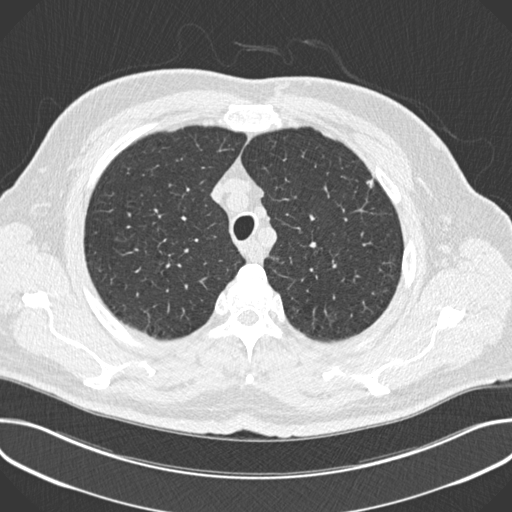
Chest CT (low-dose screening protocol), one axial image. Baseline screening round. Lung window (W 1500 / L -600 HU). 2 mm slice thickness. Standard (soft-tissue) reconstruction kernel (B30f). Slice 51 of 245 in the series. 512 × 512 image matrix, field of view 380 × 380 mm. Male participant, aged 63 years at enrolment. Current smoker at enrolment.
- Lesion marked by an expert reader, bounding box [x1, y1, x2, y2] px = [354, 170, 383, 199].
- The screening reader recorded 2 non-calcified nodules or masses ≥4 mm on this exam; which of them this box marks is not recorded.